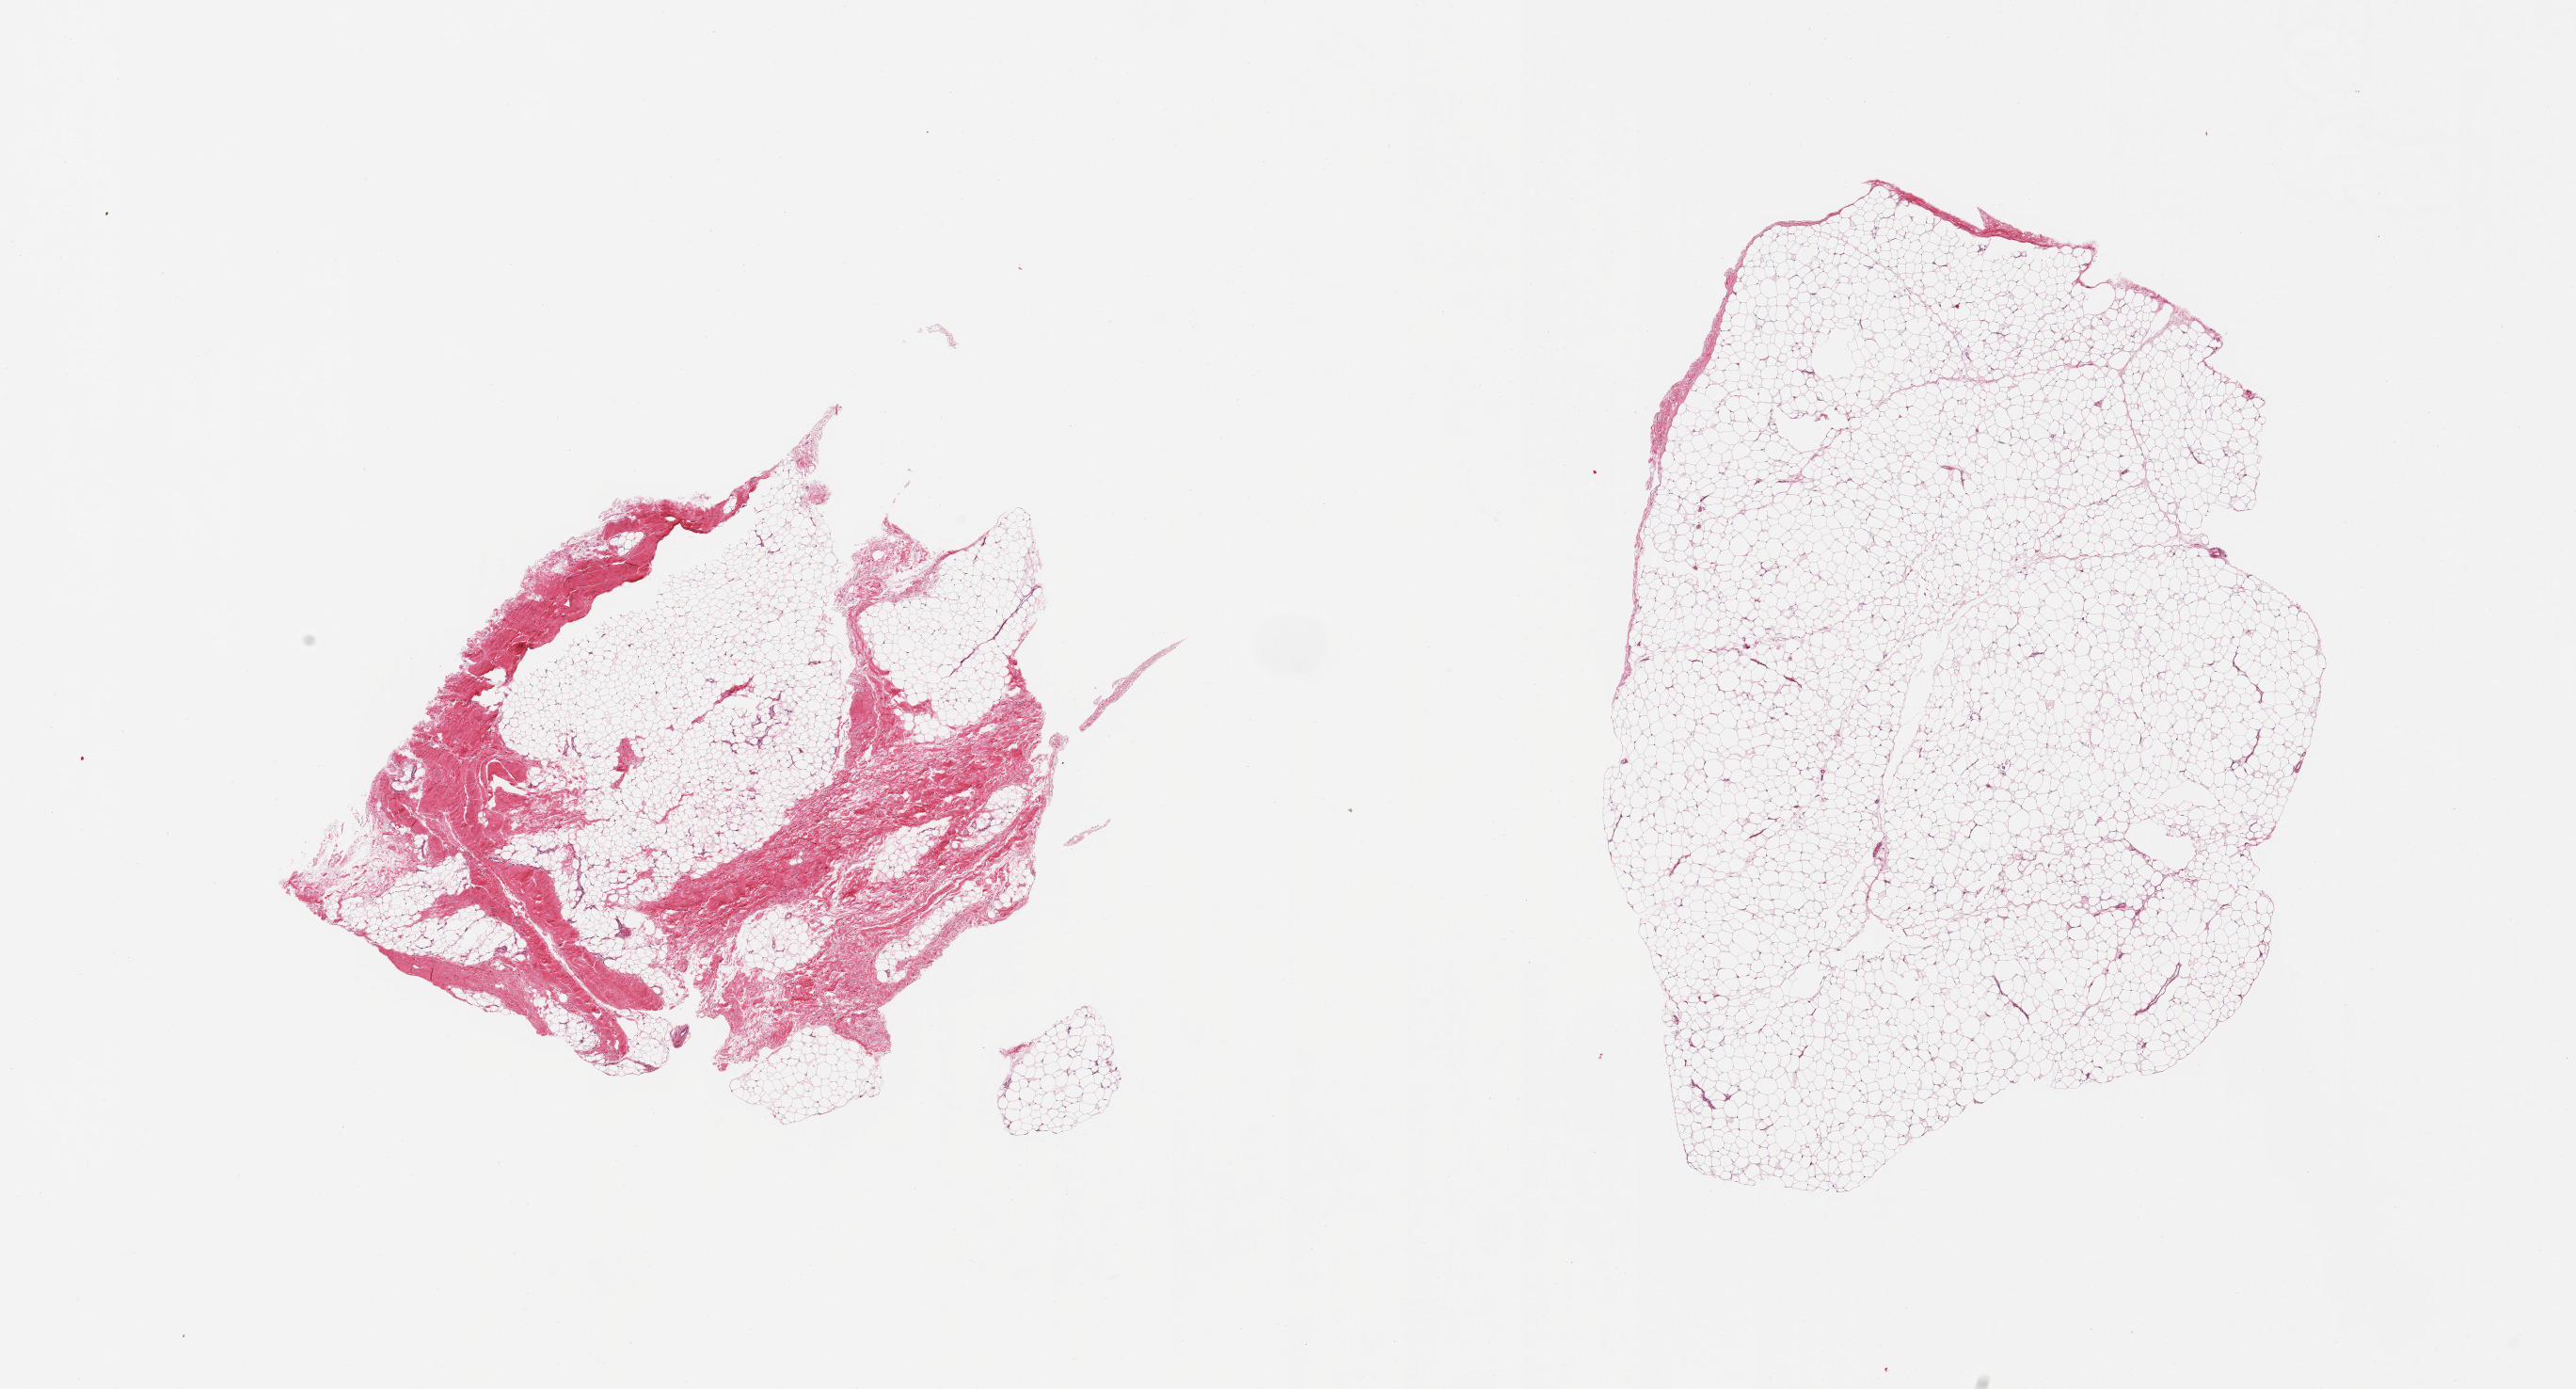
Digitized hematoxylin and eosin (H&E)-stained section, brightfield — a low-resolution overview of the entire scanned area, about 21.7 x 11.7 mm. PAXgene-fixed, paraffin-embedded tissue. Section of adipose tissue (target tissue). Donor tissue sample. Donor: male.
* reviewer comment on this tissue sample: 2 pieces, ~30% fascia/vascular elements